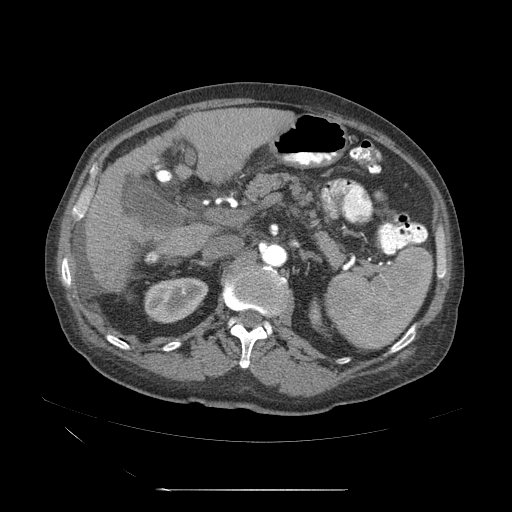
Contrast-enhanced abdominal CT (liver protocol), one axial slice. Slice 21 of 71 in the series (ordered by position). Reconstruction kernel STANDARD. 120 kVp. Soft-tissue window (W 400 / L 40 HU). 512 × 512 image matrix. Case-level facts recorded for this patient, not image findings: diagnosis: hepatocellular carcinoma (patient treated with transarterial chemoembolisation; whether this scan precedes or follows treatment is not stated here); TNM stage (as recorded): Stage-II; Child-Pugh class: A; tumour nodularity: multinodular; tumour size: 1 cm.
Structures marked on this image (semi-automatic segmentation, software-assisted and operator-edited):
- abdominal aorta: box from (x=261, y=243) to (x=286, y=269) px
- liver parenchyma outside the tumour (the mass and vessels are separate outlines, so this box may not span the whole liver): (x=83, y=128)–(x=235, y=297)
- liver vessels: (x=201, y=207)–(x=250, y=262)